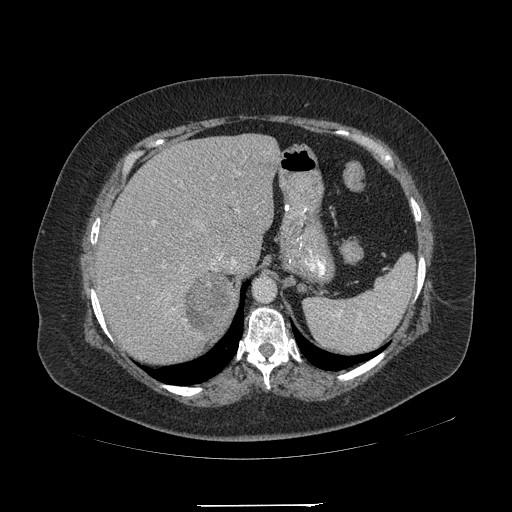
Contrast-enhanced abdominal CT, one axial slice; 120 kVp; soft-tissue window (W 400 / L 40 HU); 1.25 mm slice thickness; 512 × 512 image matrix, field of view 453 × 453 mm. Female patient, age 55 years. From the clinical record (not read from this slice): diagnosis: adrenocortical carcinoma; tumour side: right adrenal; tumour size at pathology: 11 cm; Ki-67 index: 20 %; stage (as recorded): 2.
Outlined on this slice (semi-automatic segmentation, software-assisted and operator-edited):
- mass: box from (x=187, y=273) to (x=235, y=335) px